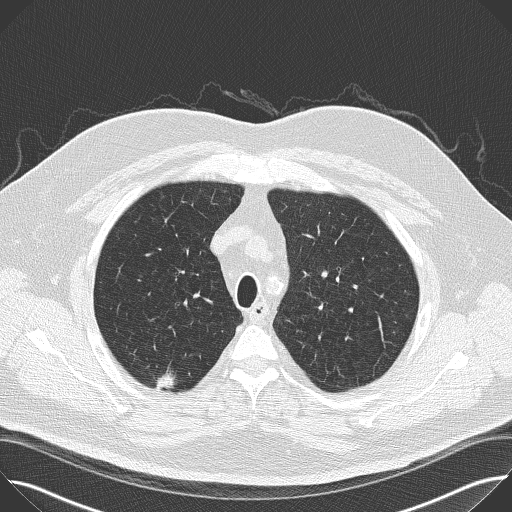
Axial slice from a low-dose chest CT screening exam; baseline screening round; lung window (W 1500 / L -600 HU); 2 mm slice thickness; lung (sharp) reconstruction kernel (B50f); 120 kVp; slice 126 of 160 in the series. Male participant, aged 65 years at enrolment. Former smoker at enrolment.
Lesion marked by an expert reader, box from (x=142, y=366) to (x=190, y=404) px. The screening reader recorded 2 non-calcified nodules or masses ≥4 mm on this exam (right upper lobe, right upper lobe); which of them this box marks is not recorded. Lung cancer was diagnosed 47 days after this screen: bronchiolo-alveolar adenocarcinoma, NOS, right upper lobe, moderately differentiated (G2), stage IIA (AJCC 6th edition), 14 mm at pathology.